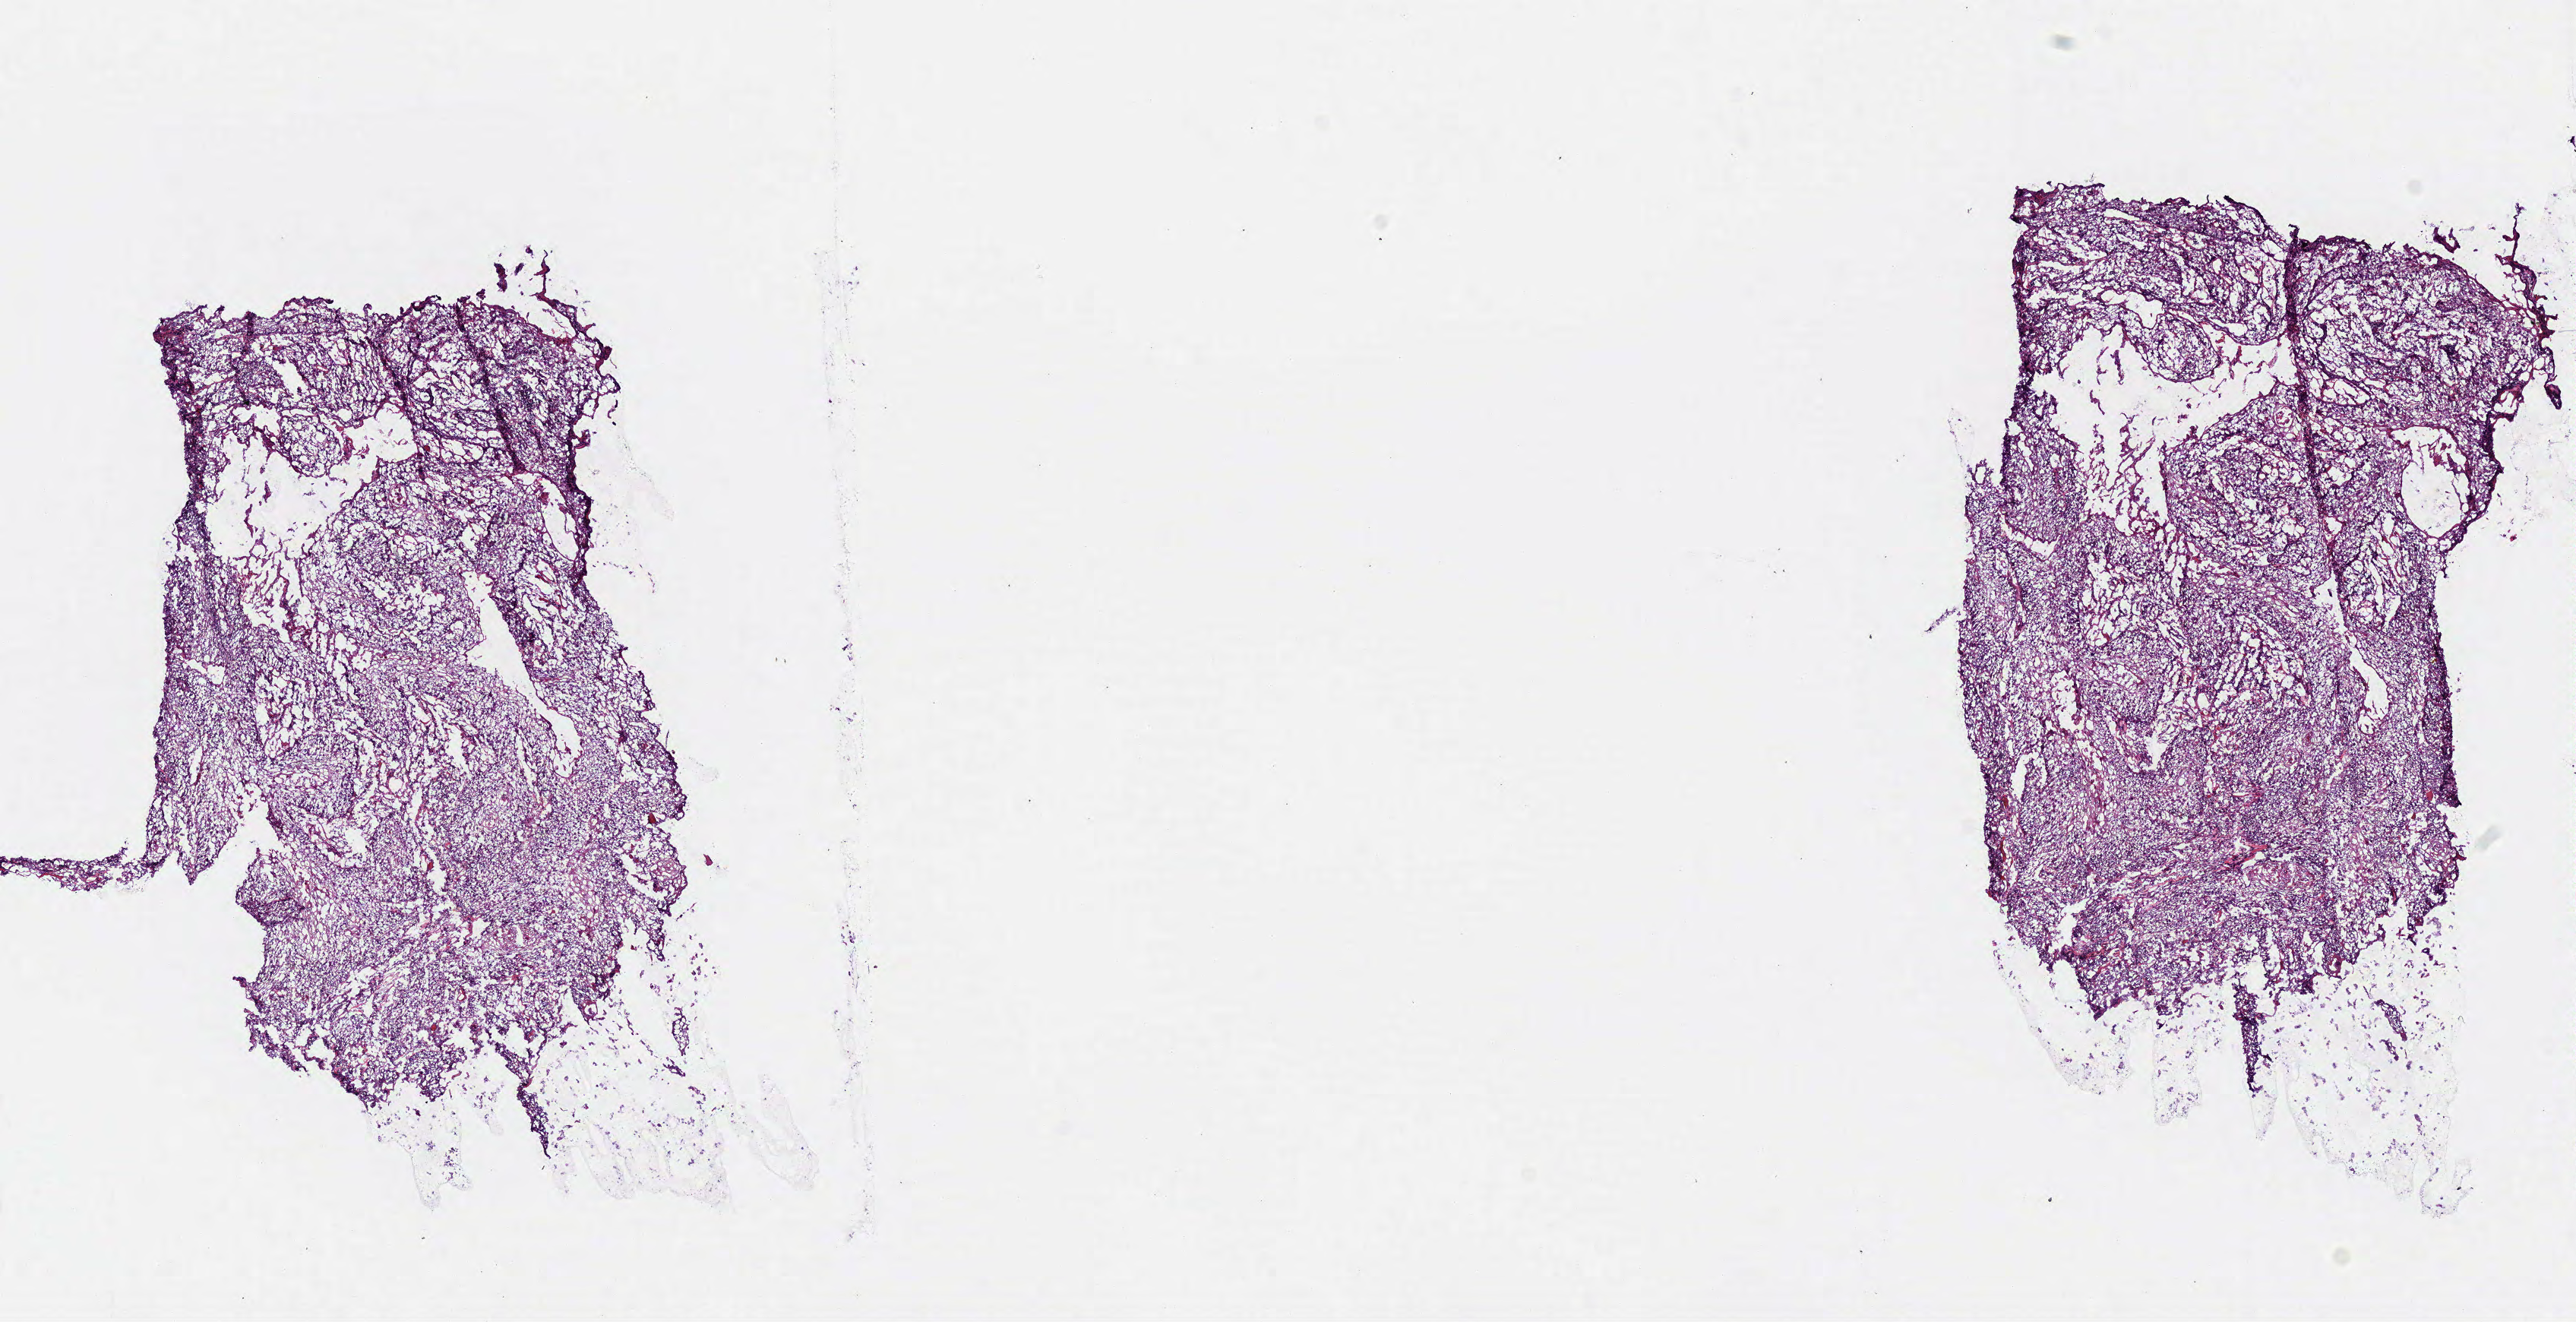
Hematoxylin and eosin (H&E) stained whole-slide image, whole scanned area (about 13.4 x 6.9 mm) shown as a low-resolution overview, frozen section from the top of the tissue portion, head and neck, primary tumour sample. Male patient; age at initial diagnosis 60 years. Histologic grade: G2 (moderately differentiated). Pathologist review of this section (percent, as recorded): tumour cells 90%, tumour nuclei 80%, normal cells 0%, stromal cells 10%, necrosis 0%.
Diagnosis: Squamous cell carcinoma, NOS. AJCC pathologic stage: IVA.